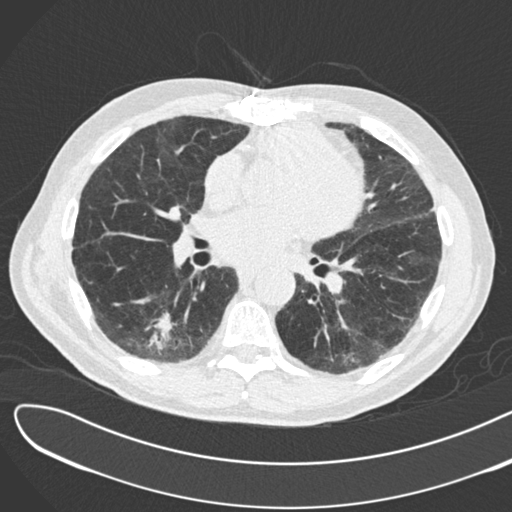
Low-dose screening chest CT, one axial slice. Position 83 of 183 along the scan axis. Reconstruction kernel B30f. 120 kVp. Lung window (W 1500 / L -600 HU). 512 × 512 image matrix, field of view 370 × 370 mm.
Outlined on this slice (outlined manually by an expert reader):
- lesion 1 (tumor, lower lobe of right lung): bounding box <146,312,171,355> (left, top, right, bottom; pixels)